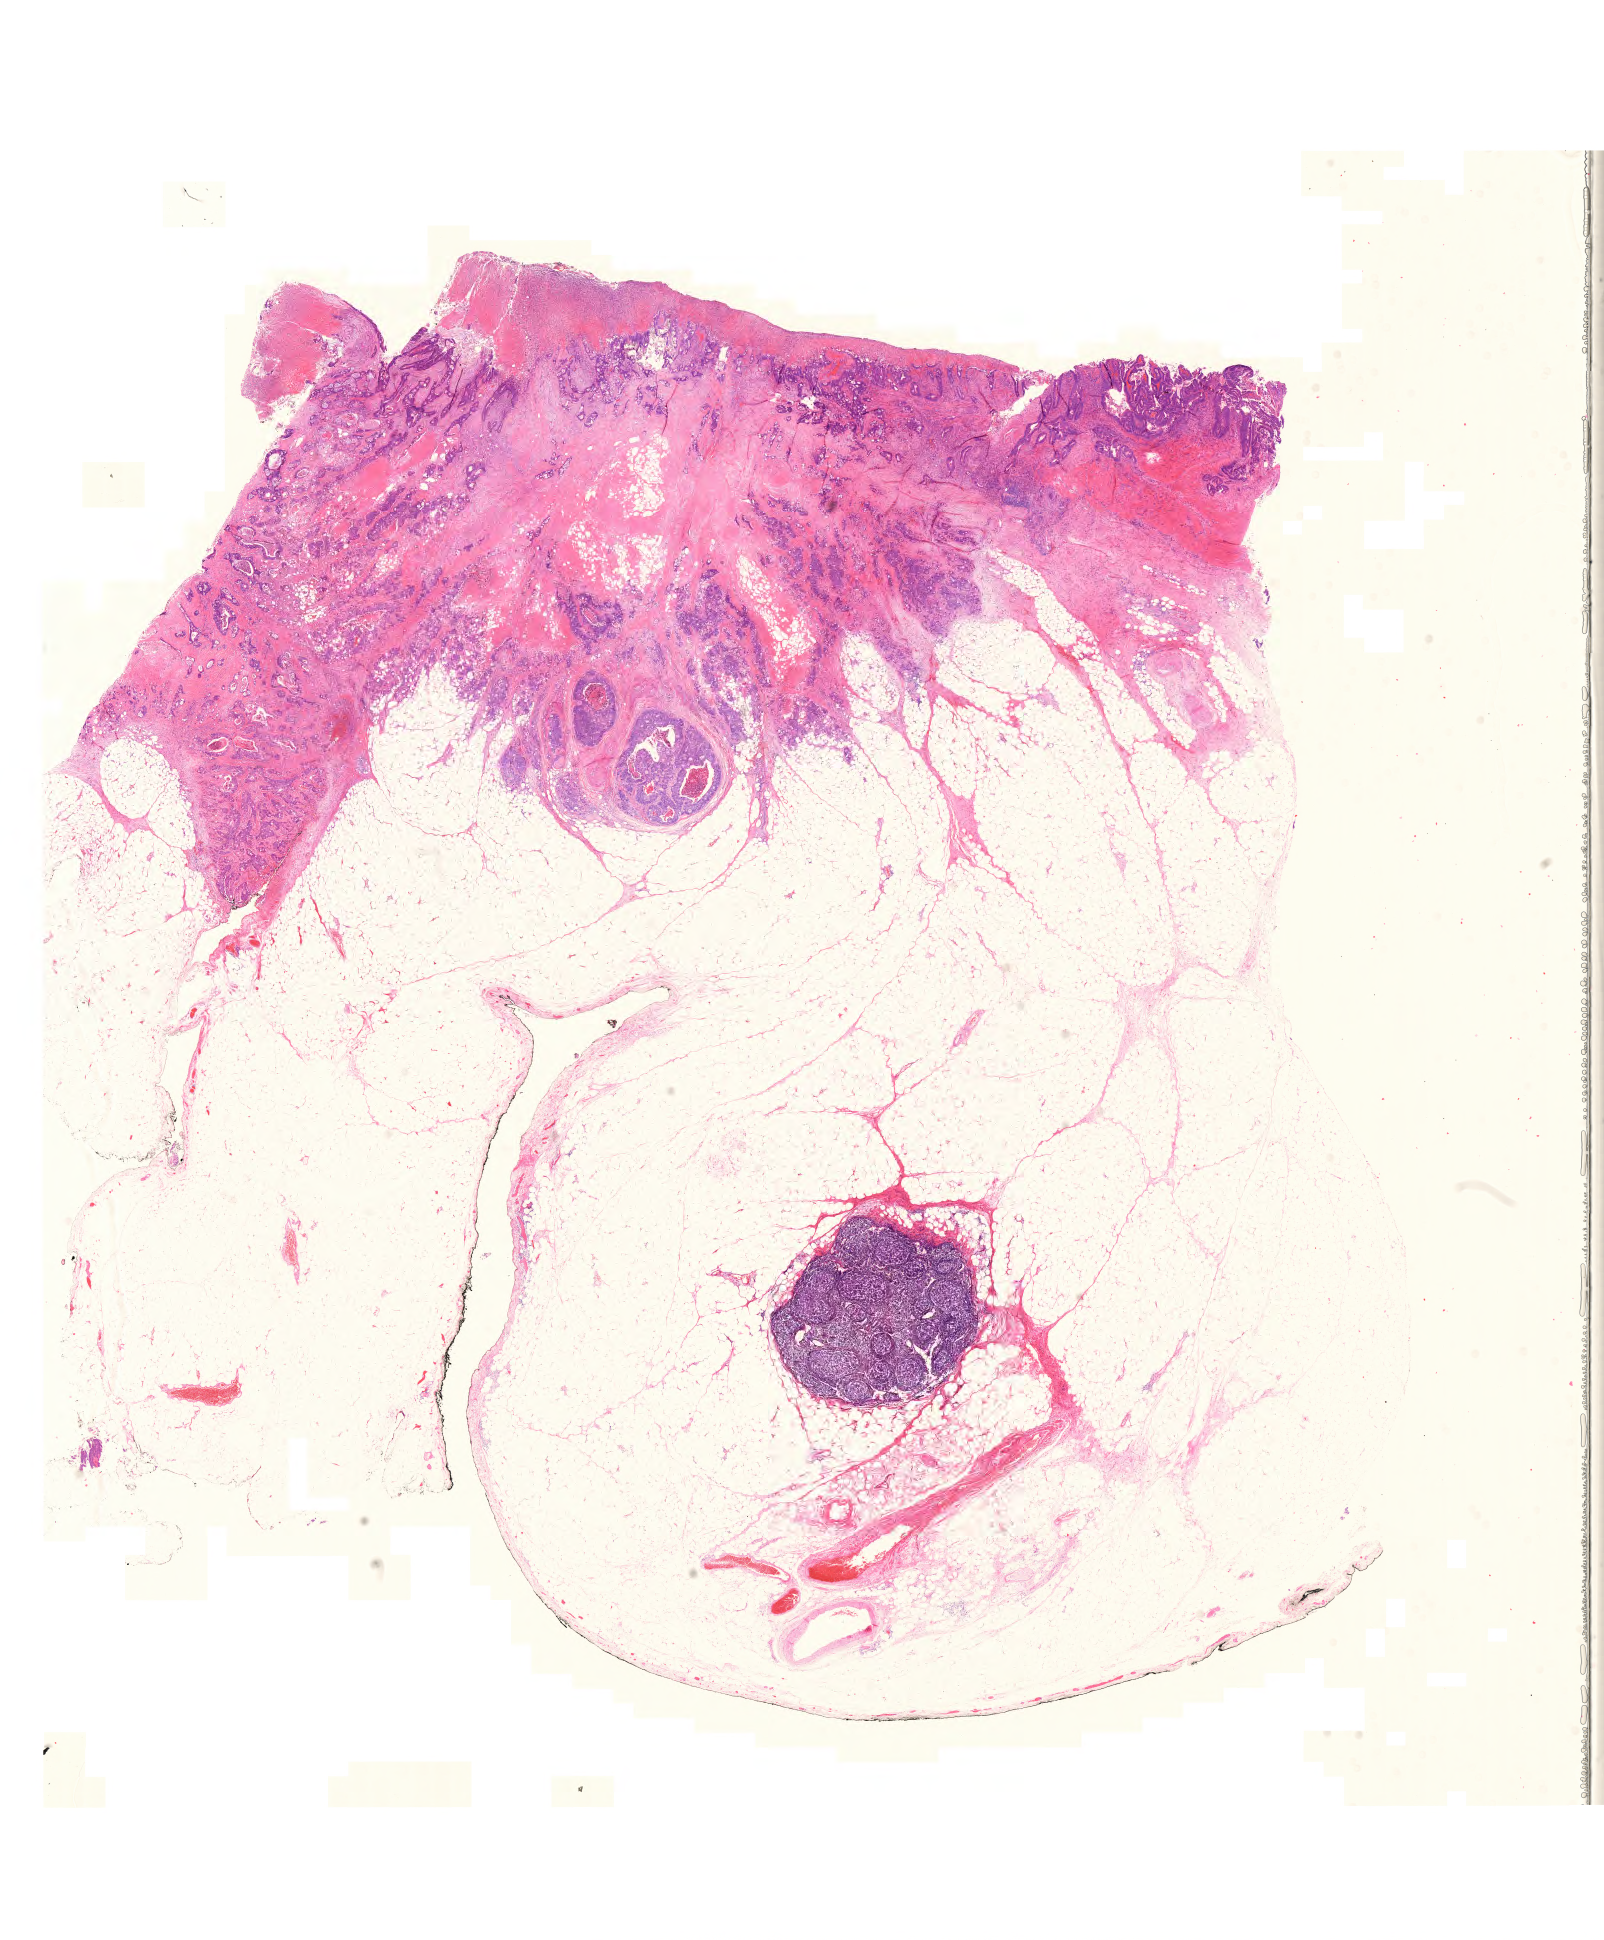
Whole-slide histology image, Hematoxylin and eosin (H&E) stained, a low-resolution overview of the entire scanned area, about 23.9 x 28.9 mm (slide scanned at 20x). Formalin-fixed paraffin-embedded (FFPE) diagnostic section. Sample: primary tumour, uterus. Female patient; age at initial diagnosis 54 years. Histologic grade: G1 (well differentiated).
FIGO stage: I. Pathologic diagnosis: Endometrioid adenocarcinoma, NOS (endometrium).